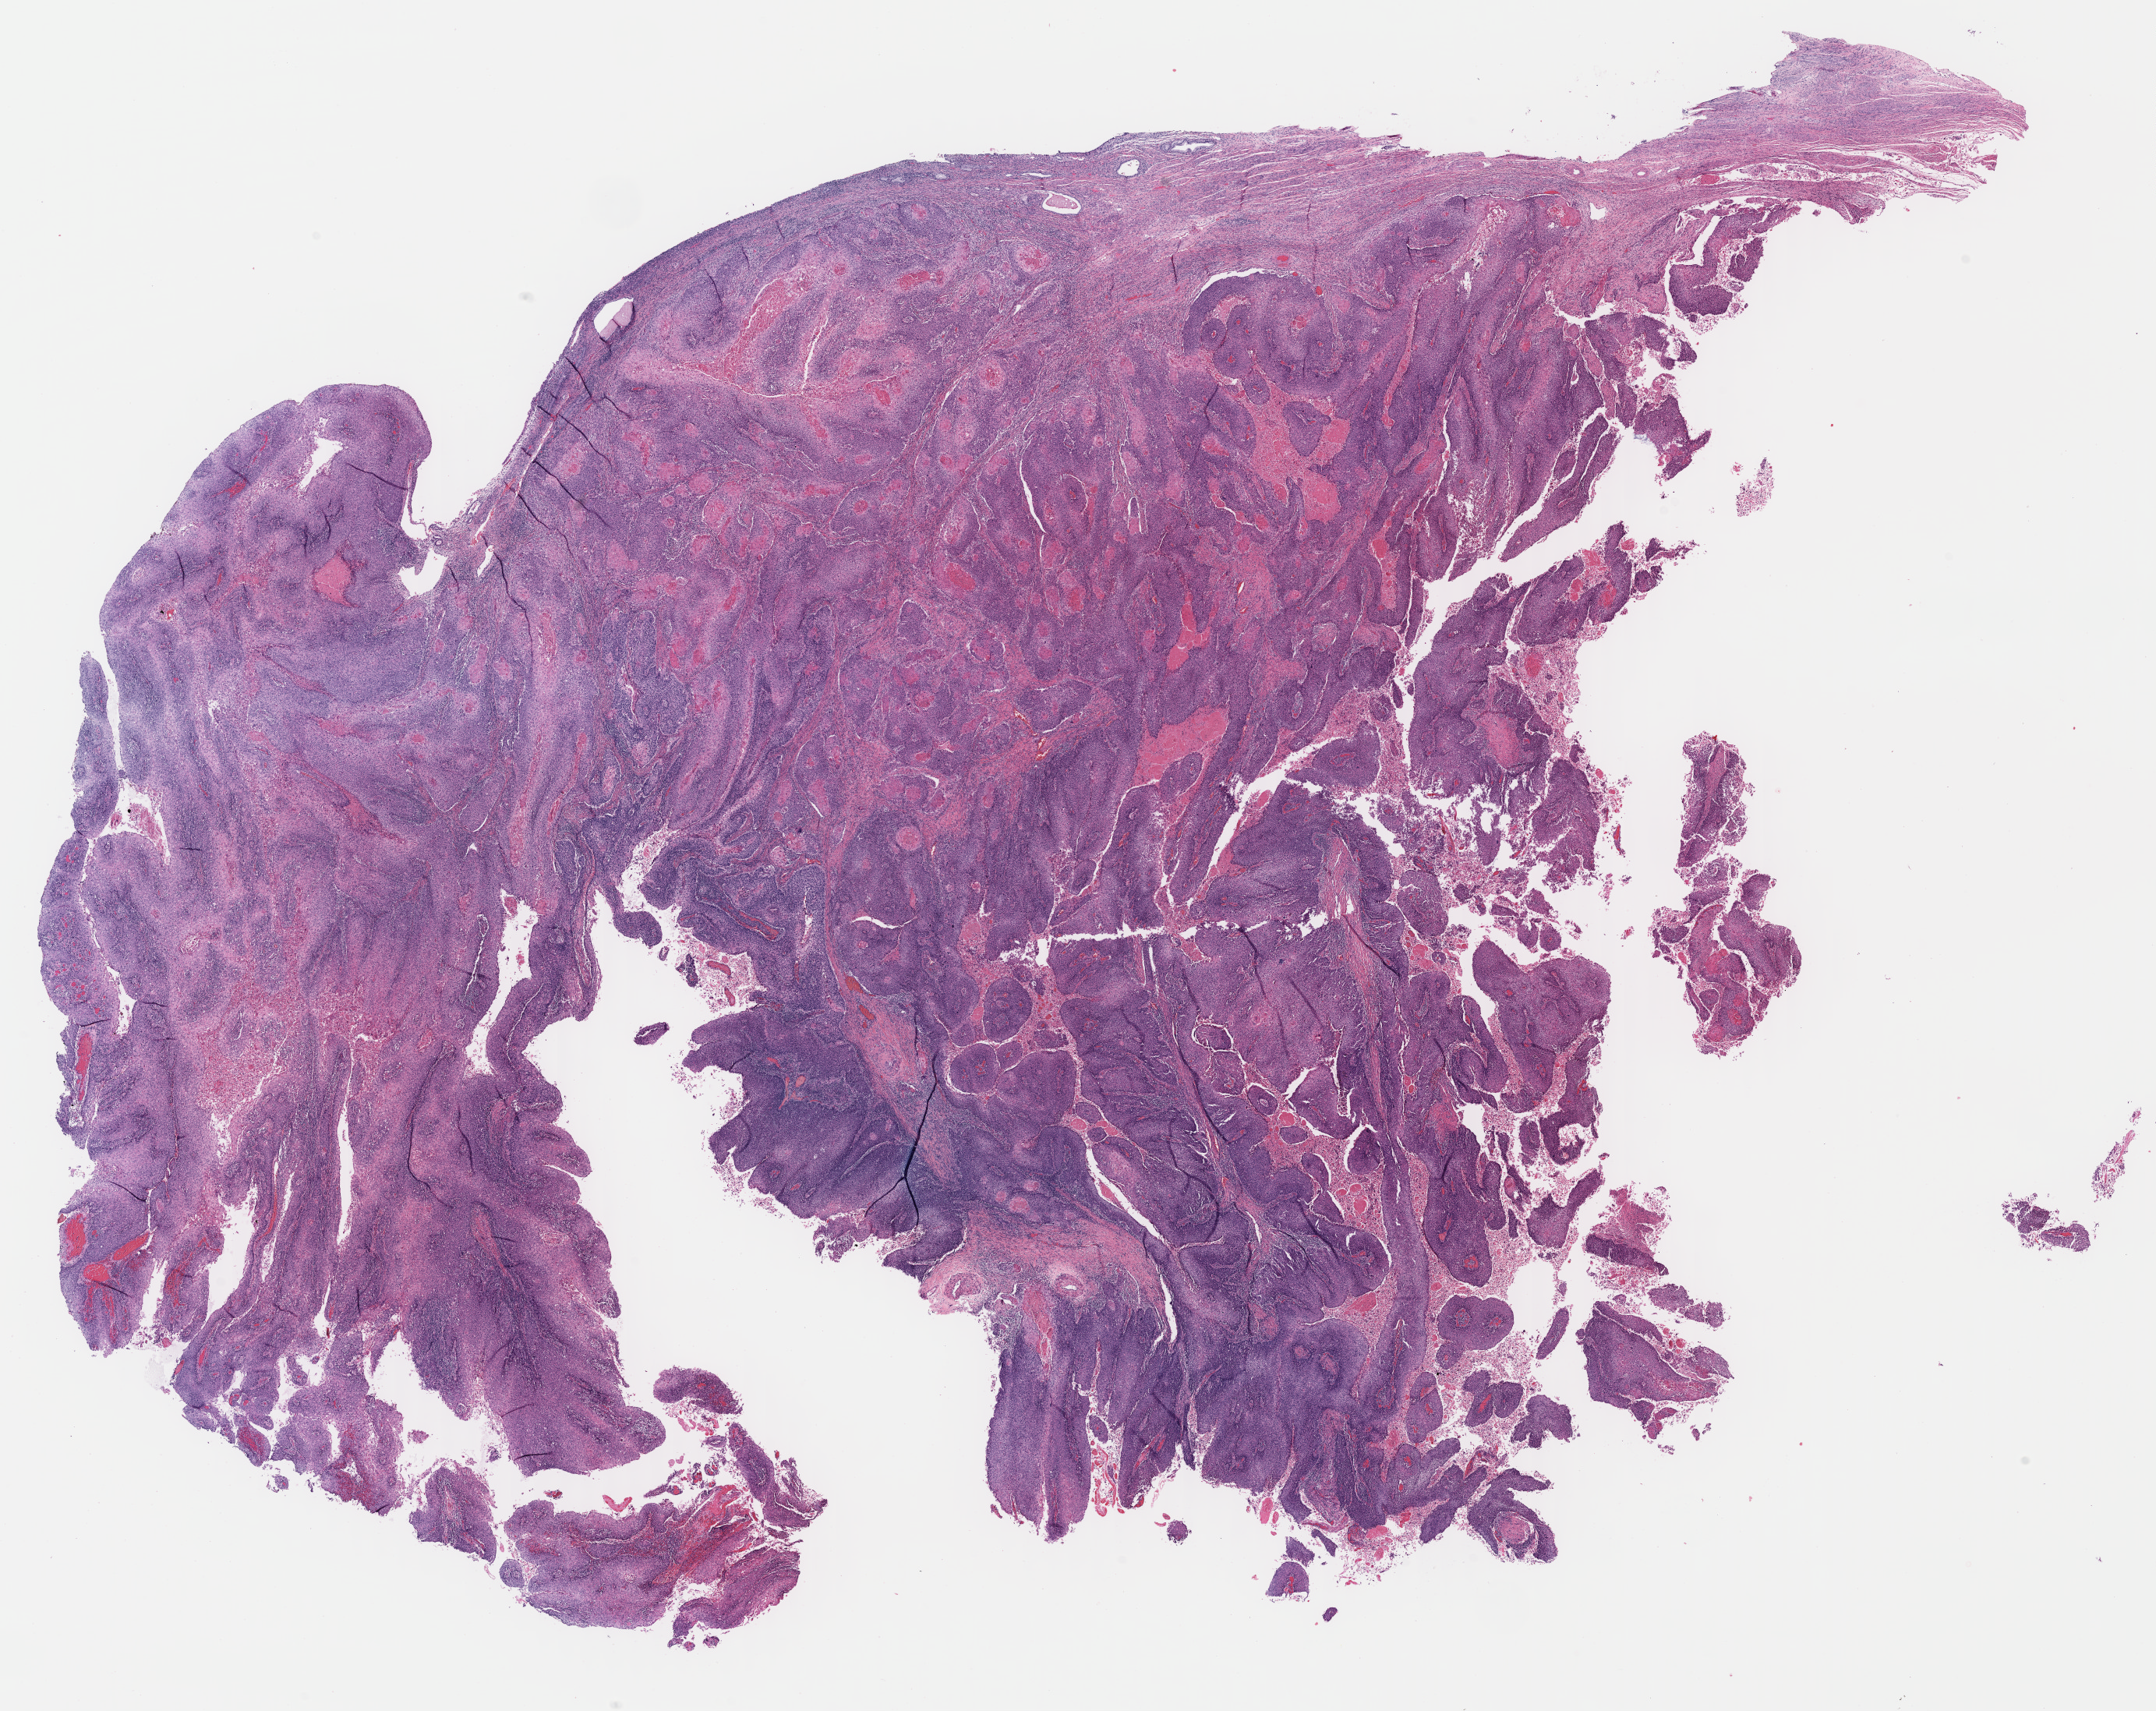
Digitized H&E tissue section (whole slide), low-resolution overview of the scanned area, about 21.7 x 17.3 mm, formalin-fixed paraffin-embedded (FFPE) diagnostic section, sample: primary tumour, cervix. Female patient; age at initial diagnosis 68 years. Histologic grade: G1 (well differentiated).
• FIGO stage: IIA2
• histologic diagnosis: Squamous cell carcinoma, keratinizing, NOS (cervix uteri)